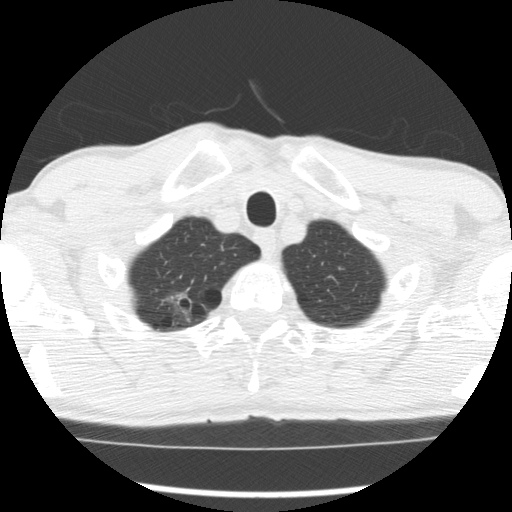
Chest CT (low-dose screening protocol), one axial image, first (baseline) screen, lung window (W 1500 / L -600 HU), 2.5 mm slice thickness, slice 22 of 277 in the series. Male participant, aged 66 years at enrolment. Former smoker at enrolment.
- Expert-annotated lung lesion, bounding box [x1, y1, x2, y2] px = [149, 284, 205, 334].
- The screening reader recorded 4 non-calcified nodules or masses ≥4 mm on this exam (right upper lobe, right upper lobe, right upper lobe, left lower lobe); which of them this box marks is not recorded.
- Later outcome: lung cancer diagnosed 503 days after this screen — adenocarcinoma, NOS, right upper lobe, undifferentiated (G4), stage IA (AJCC 6th edition), 20 mm at pathology.